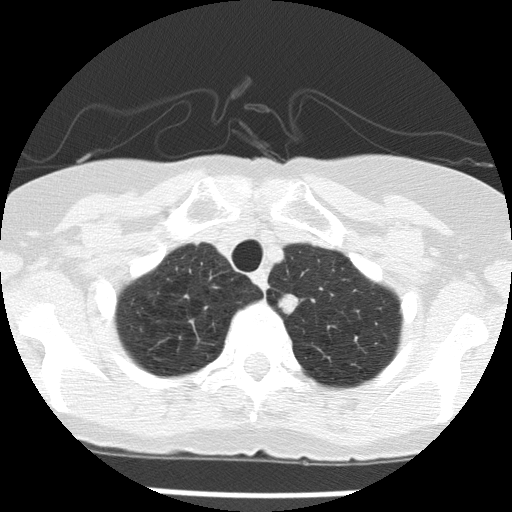
Low-dose screening chest CT, one axial slice. Position 125 of 143 along the scan axis. Reconstruction kernel FC51. 120 kVp. Lung window (W 1500 / L -600 HU). 2 mm slice thickness. 512 × 512 image matrix, field of view 276 × 276 mm.
Outlined on this slice (outlined manually by an expert reader):
- lesion 1 (tumor, upper lobe of left lung): bounding box (x1, y1, x2, y2) in pixels: (278, 294, 299, 314)